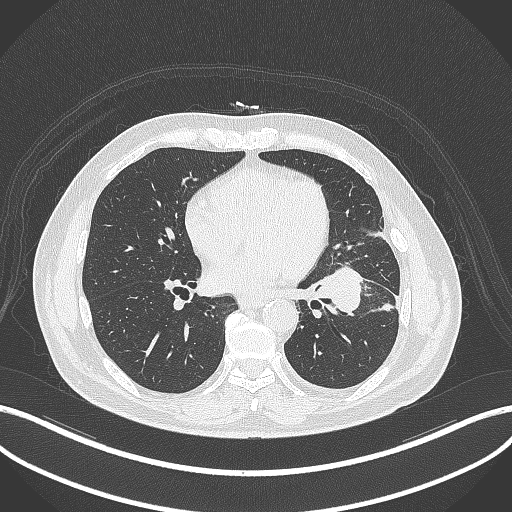
Chest CT, one axial slice. Slice 156 of 230 in the series (ordered by position). Reconstruction kernel B70f. Lung window (W 1500 / L -600 HU). 512 × 512 image matrix, field of view 400 × 400 mm. Male patient, age 68 years. From the clinical record (not read from this slice): clinical TNM (as recorded): T2b N0 M0.
Annotated regions visible in this slice (bounding box drawn by a radiologist):
- lung tumour (recorded histology: squamous cell carcinoma): bounding box <313,262,365,318> (left, top, right, bottom; pixels)